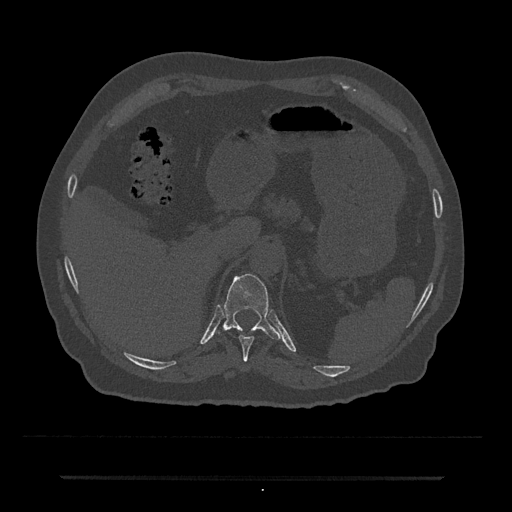
CT including the spine, one axial slice. Slice 196 of 797 in the series (ordered by position). Bone window (W 1800 / L 400 HU). 512 × 512 image matrix. Patient: male, 69 years. From the clinical record (not read from this slice): primary cancer: prostate.
Annotated regions visible in this slice (semi-automatic segmentation, software-assisted and operator-edited):
- T10 vertebra: bounding box [x1, y1, x2, y2] px = [238, 335, 255, 361]
- T11 vertebra: [223, 273, 282, 340]